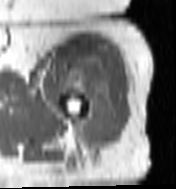
MRI of an extremity soft-tissue mass, one axial slice; position 86 of 100 along the scan axis; MR volume resampled by the dataset authors to the PET/CT grid (not the native acquisition matrix); 3.27 mm slice thickness; 176 × 189 image matrix, field of view 172 × 185 mm. Female patient. From the clinical record (not read from this slice): histological type: undifferentiated – high grade; grade: high; site of the primary tumour: left thigh.
Annotated regions visible in this slice (expert contour drawn on MRI and transferred to this co-registered scan by the dataset authors):
- gross tumour volume including surrounding oedema: box from (x=69, y=61) to (x=118, y=143) px
- gross tumour volume (mass): (x=71, y=61)–(x=115, y=143)